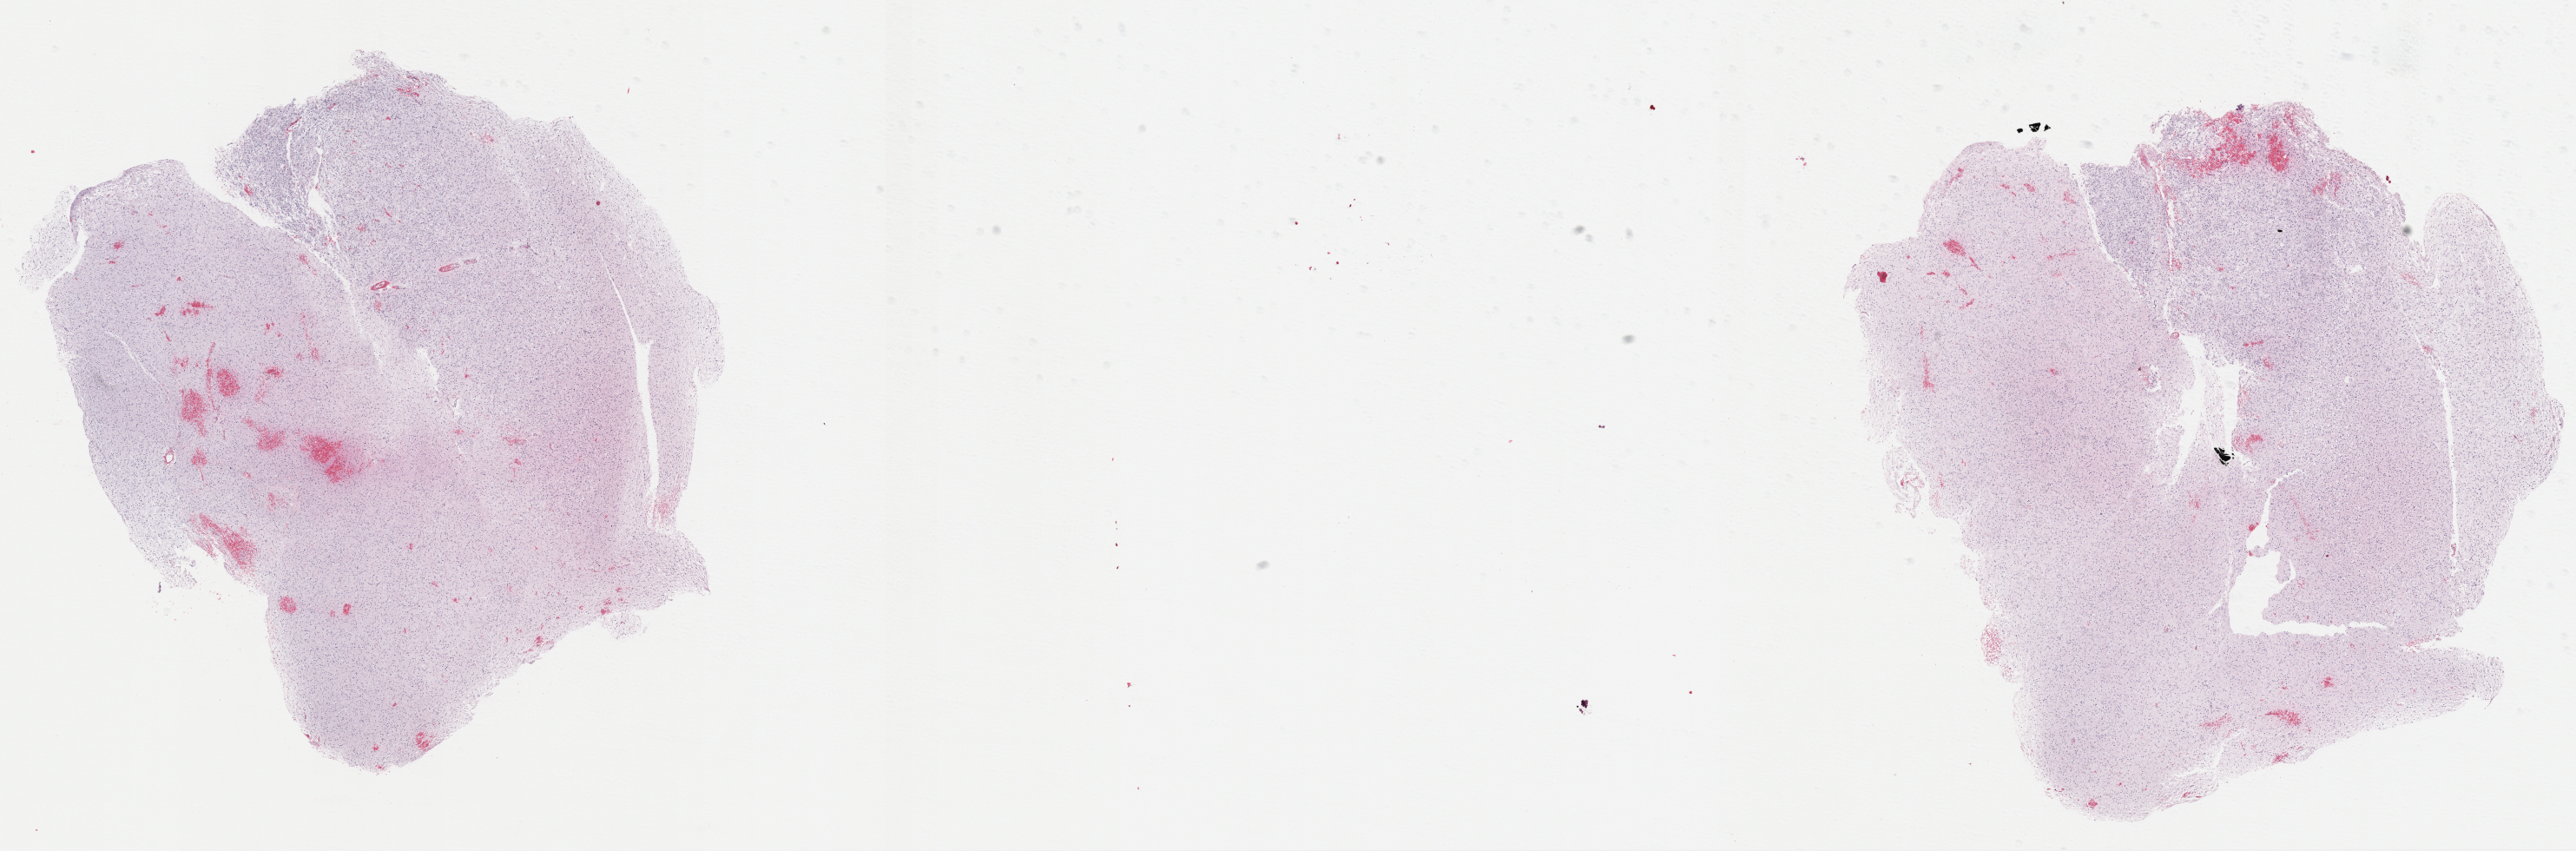
H&E-stained whole-slide image — low-resolution overview of the scanned area, about 23.9 x 7.9 mm, formalin-fixed paraffin-embedded (FFPE) diagnostic section, primary tumour sample from the brain. Male, age 35 years at initial diagnosis. Histologic grade: G2 (moderately differentiated).
• diagnosis: Oligodendroglioma, NOS (cerebrum)